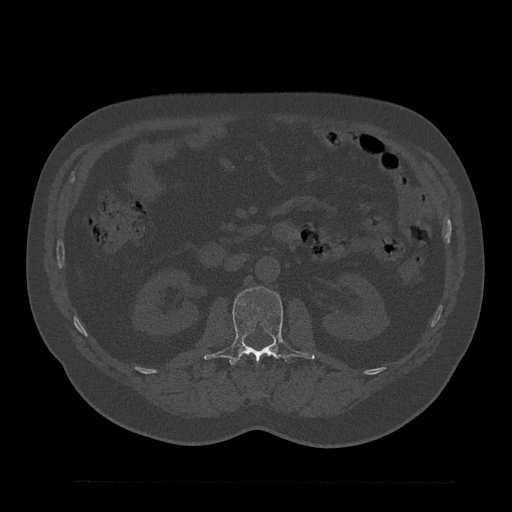
CT including the spine, one axial slice; position 107 of 797 along the scan axis; reconstruction kernel Br40s/3; 120 kVp; bone window (W 1800 / L 400 HU); 0.5 mm slice thickness; 512 × 512 image matrix. Male patient, age 61 years. From the clinical record (not read from this slice): primary cancer: prostate.
Annotated regions visible in this slice (semi-automatic segmentation, software-assisted and operator-edited):
- L1 vertebra: bounding box (x1, y1, x2, y2) in pixels: (263, 352, 273, 356)
- L2 vertebra: (204, 287, 315, 368)